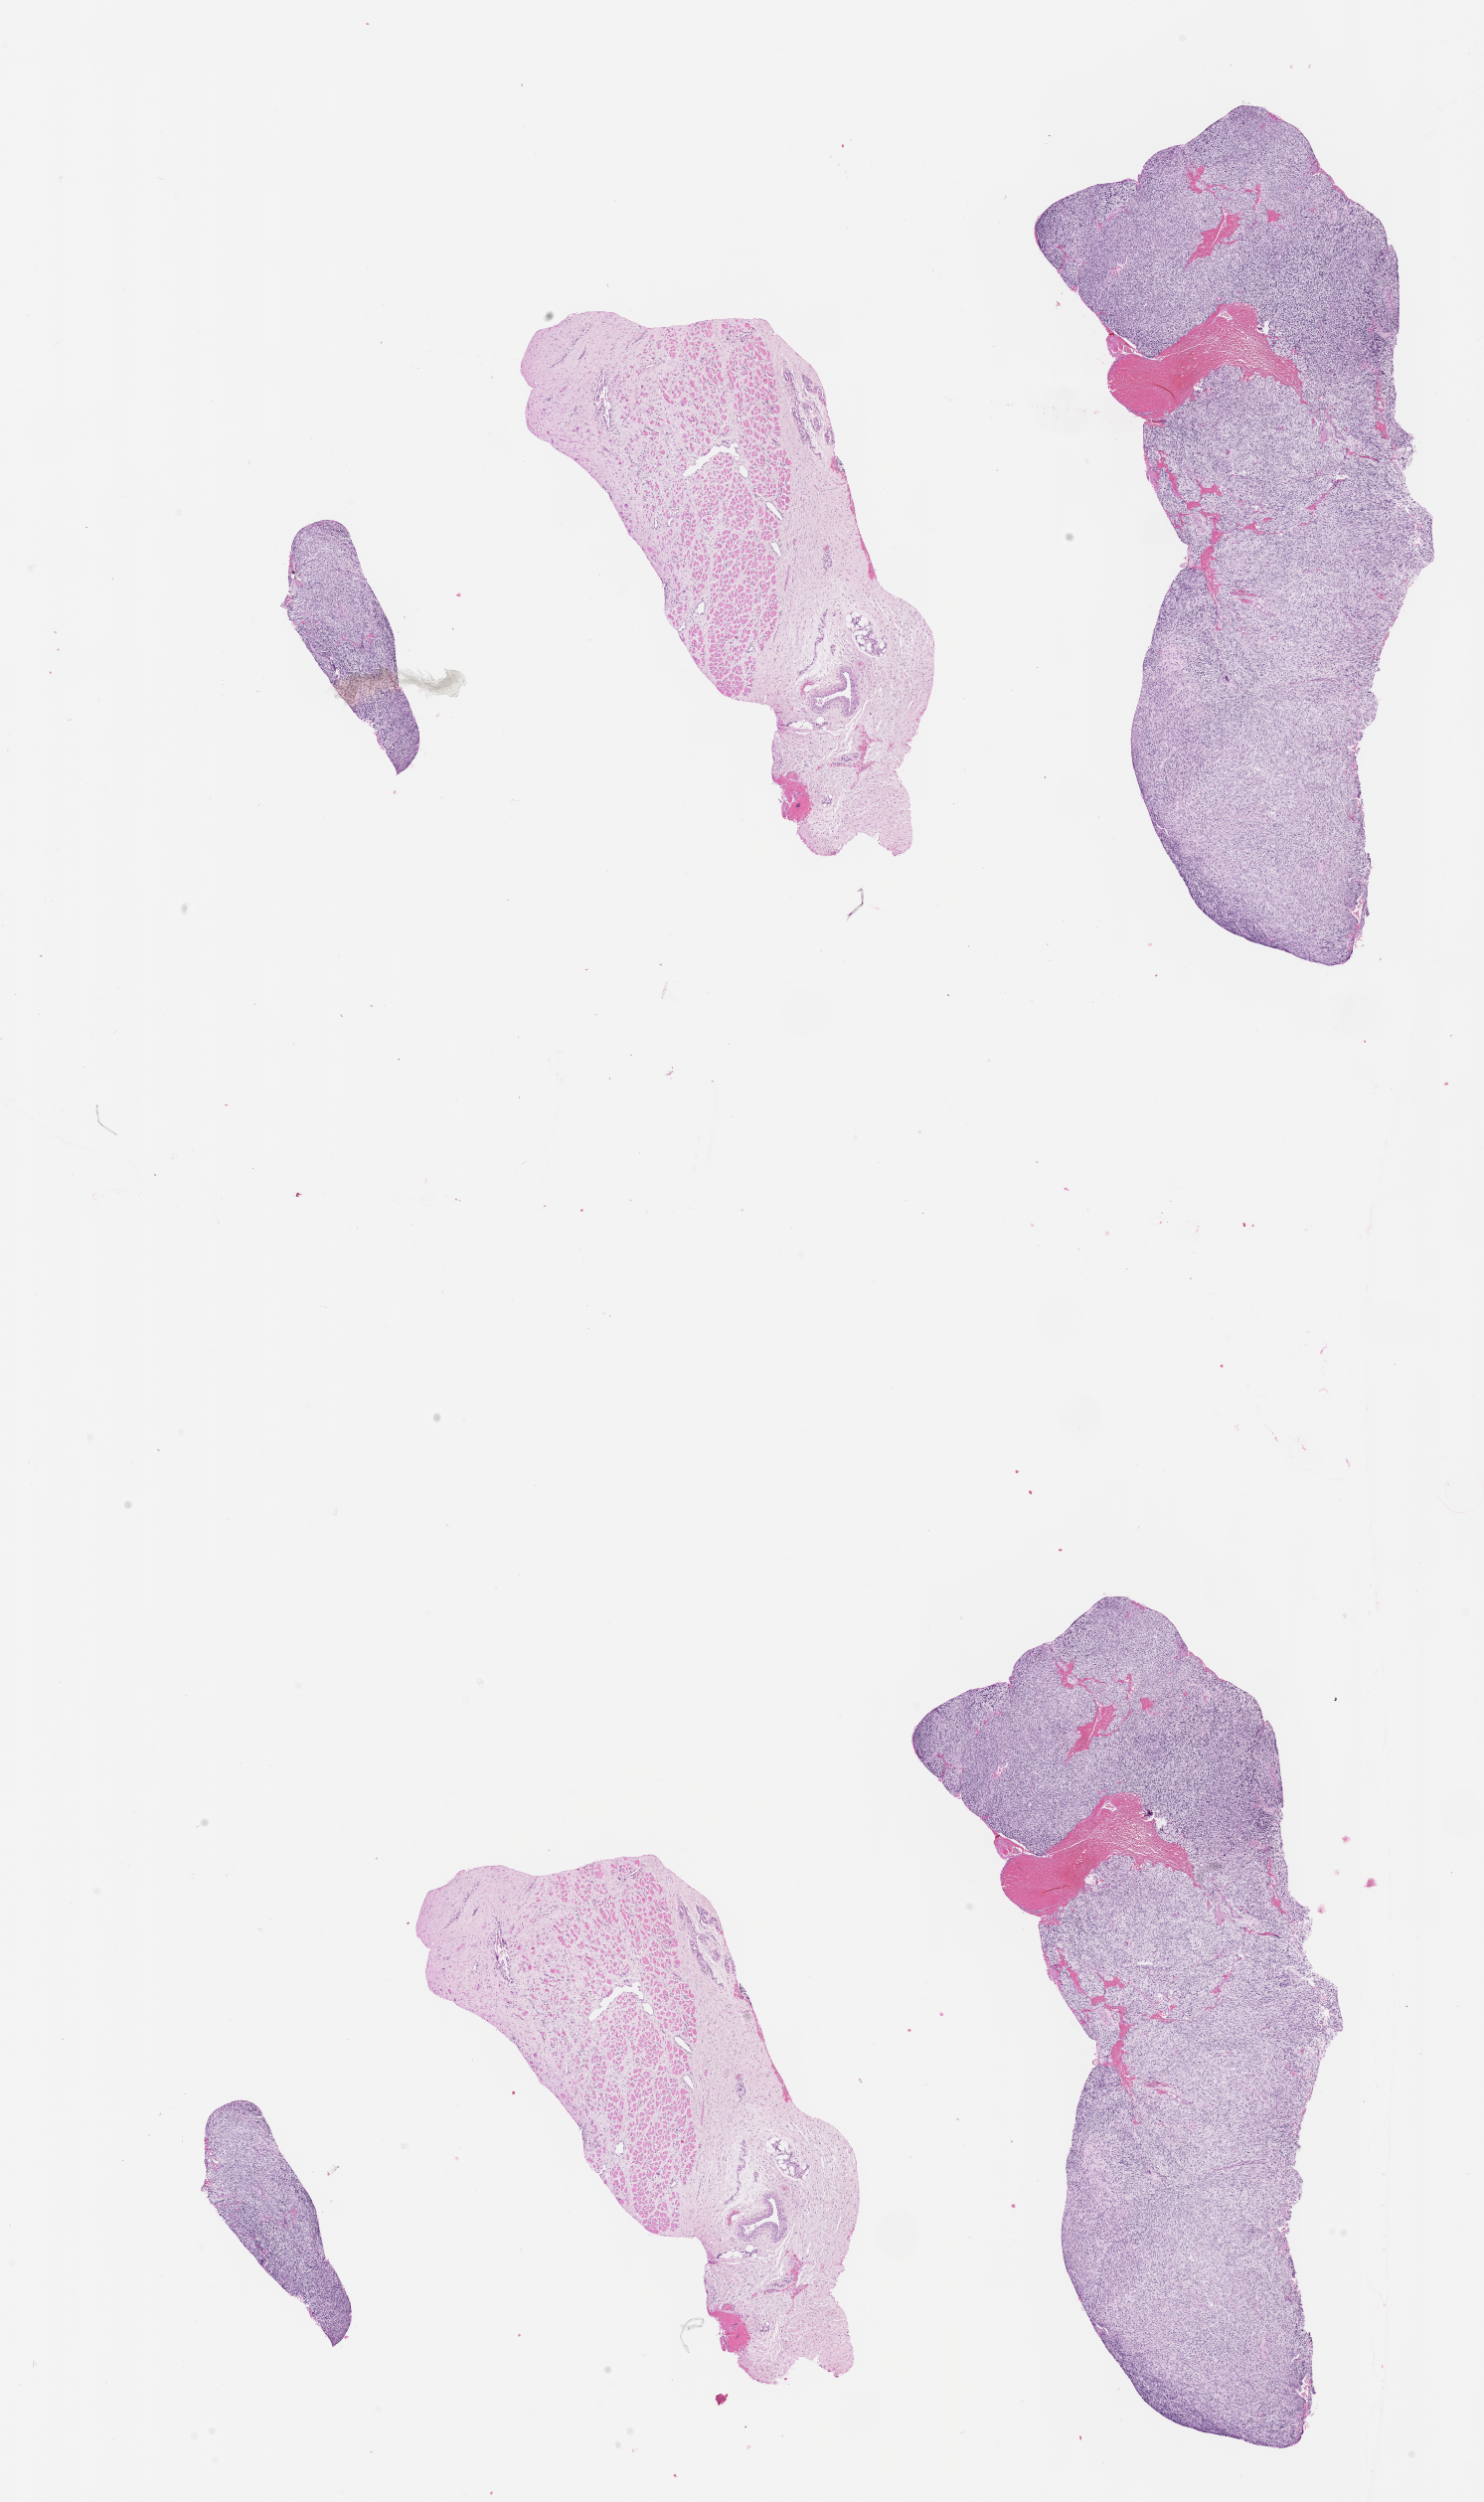
Whole-slide image, haematoxylin and eosin stain of tumor tissue — shown as a low-resolution overview of the whole scanned area (about 12.1 x 20.4 mm), formalin-fixed, paraffin-embedded (FFPE) tissue, sample anatomic site: pelvis. Male patient, age at diagnosis 2.0 years.
• primary site (case record): prostate
• stage (as recorded): 2
• diagnosis: rhabdomyosarcoma; histological classification: embryonal rhabdomyosarcoma